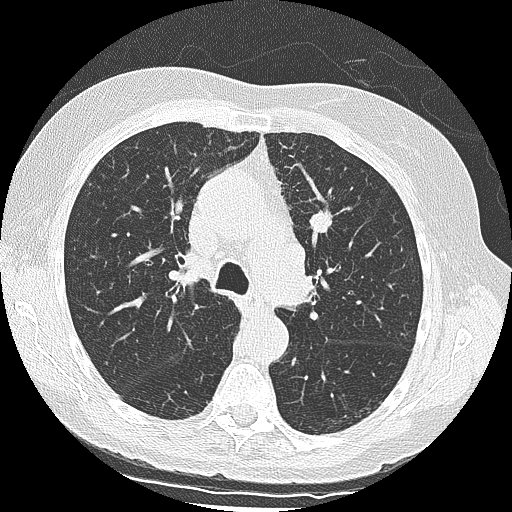
Low-dose screening chest CT, one axial slice. Slice 94 of 139 in the series (ordered by position). 120 kVp. Lung window (W 1500 / L -600 HU). 2.5 mm slice thickness. 512 × 512 image matrix.
Annotated regions visible in this slice (outlined manually by an expert reader):
- lesion 1 (tumor, upper lobe of left lung): box from (x=309, y=207) to (x=333, y=234) px